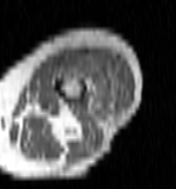
MRI of an extremity soft-tissue mass, one axial slice. MR volume resampled by the dataset authors to the PET/CT grid (not the native acquisition matrix). 176 × 189 image matrix, field of view 172 × 185 mm. Female patient. Case-level facts recorded for this patient, not image findings: histological type: undifferentiated – high grade; grade: high; site of the primary tumour: left thigh.
Outlined on this slice (expert contour drawn on MRI and transferred to this co-registered scan by the dataset authors):
- gross tumour volume including surrounding oedema: bounding box (x1, y1, x2, y2) in pixels: (64, 54, 124, 115)